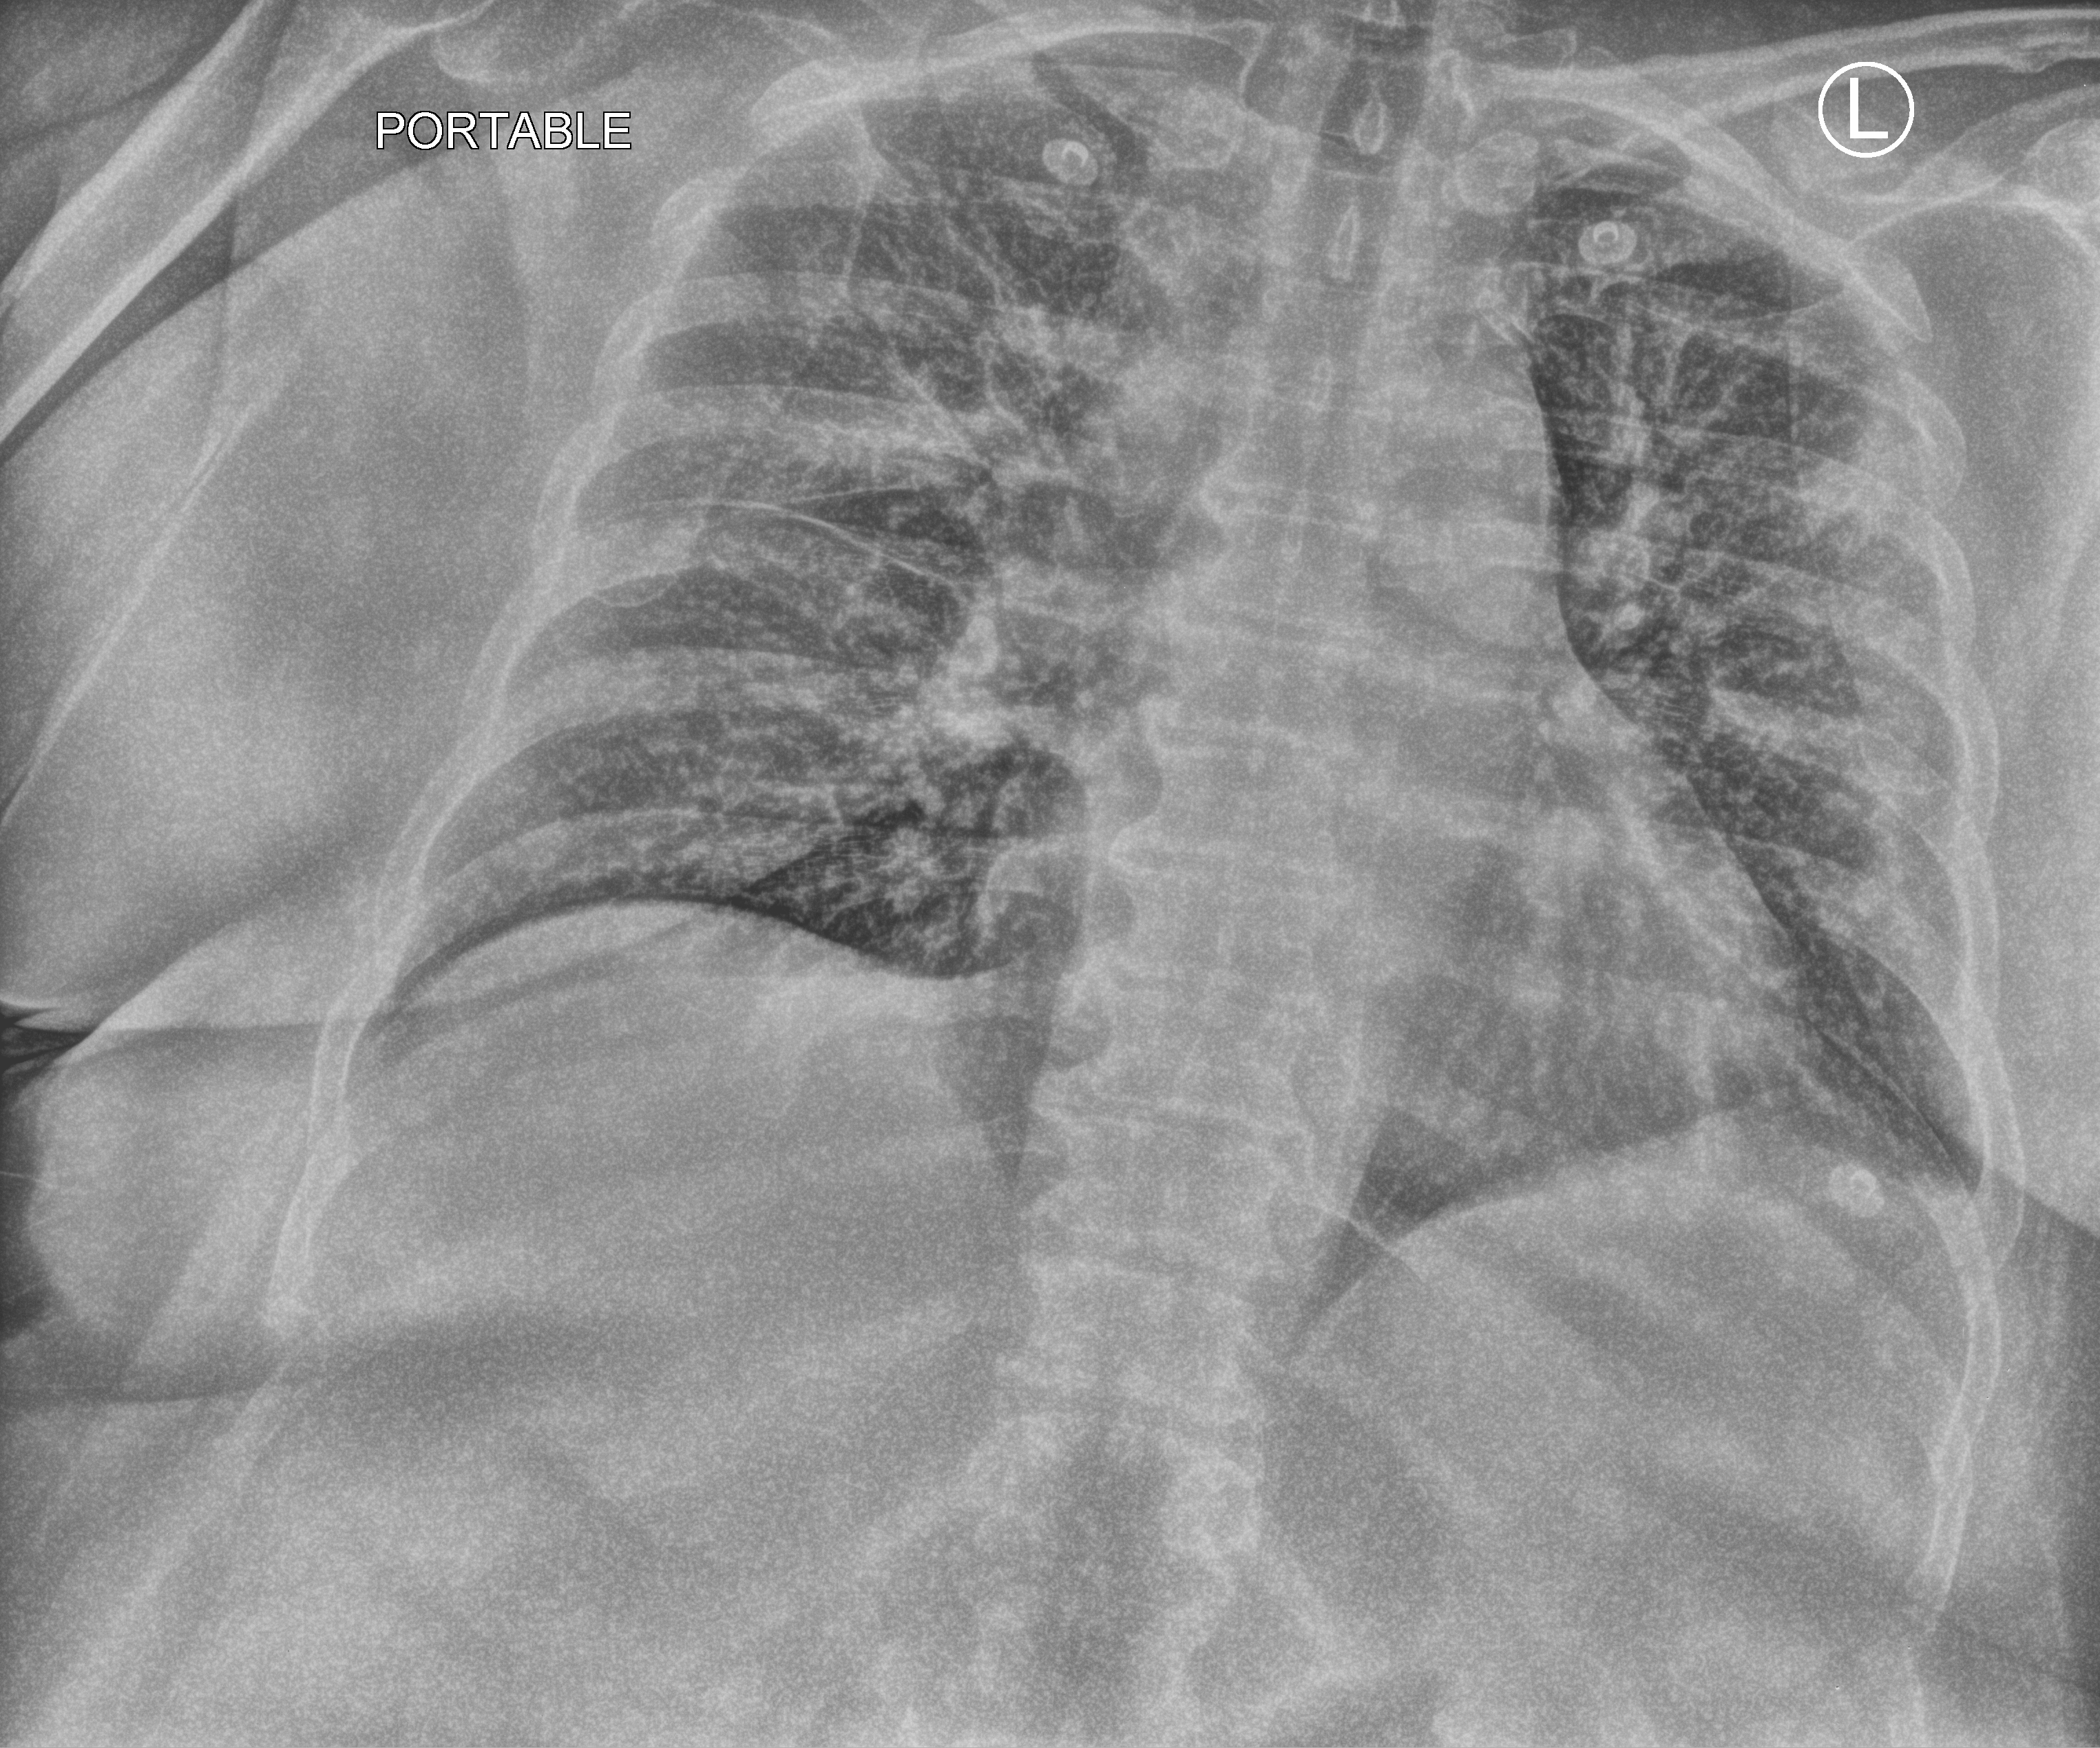
Portable chest radiograph; anteroposterior (AP) projection. Female patient hospitalised with COVID-19, age 60–74 years.
From the hospital-stay record, not from the radiograph (when in the stay this image was taken is not recorded):
- smoking status (admission record): former
- mechanically ventilated during this hospital stay: no